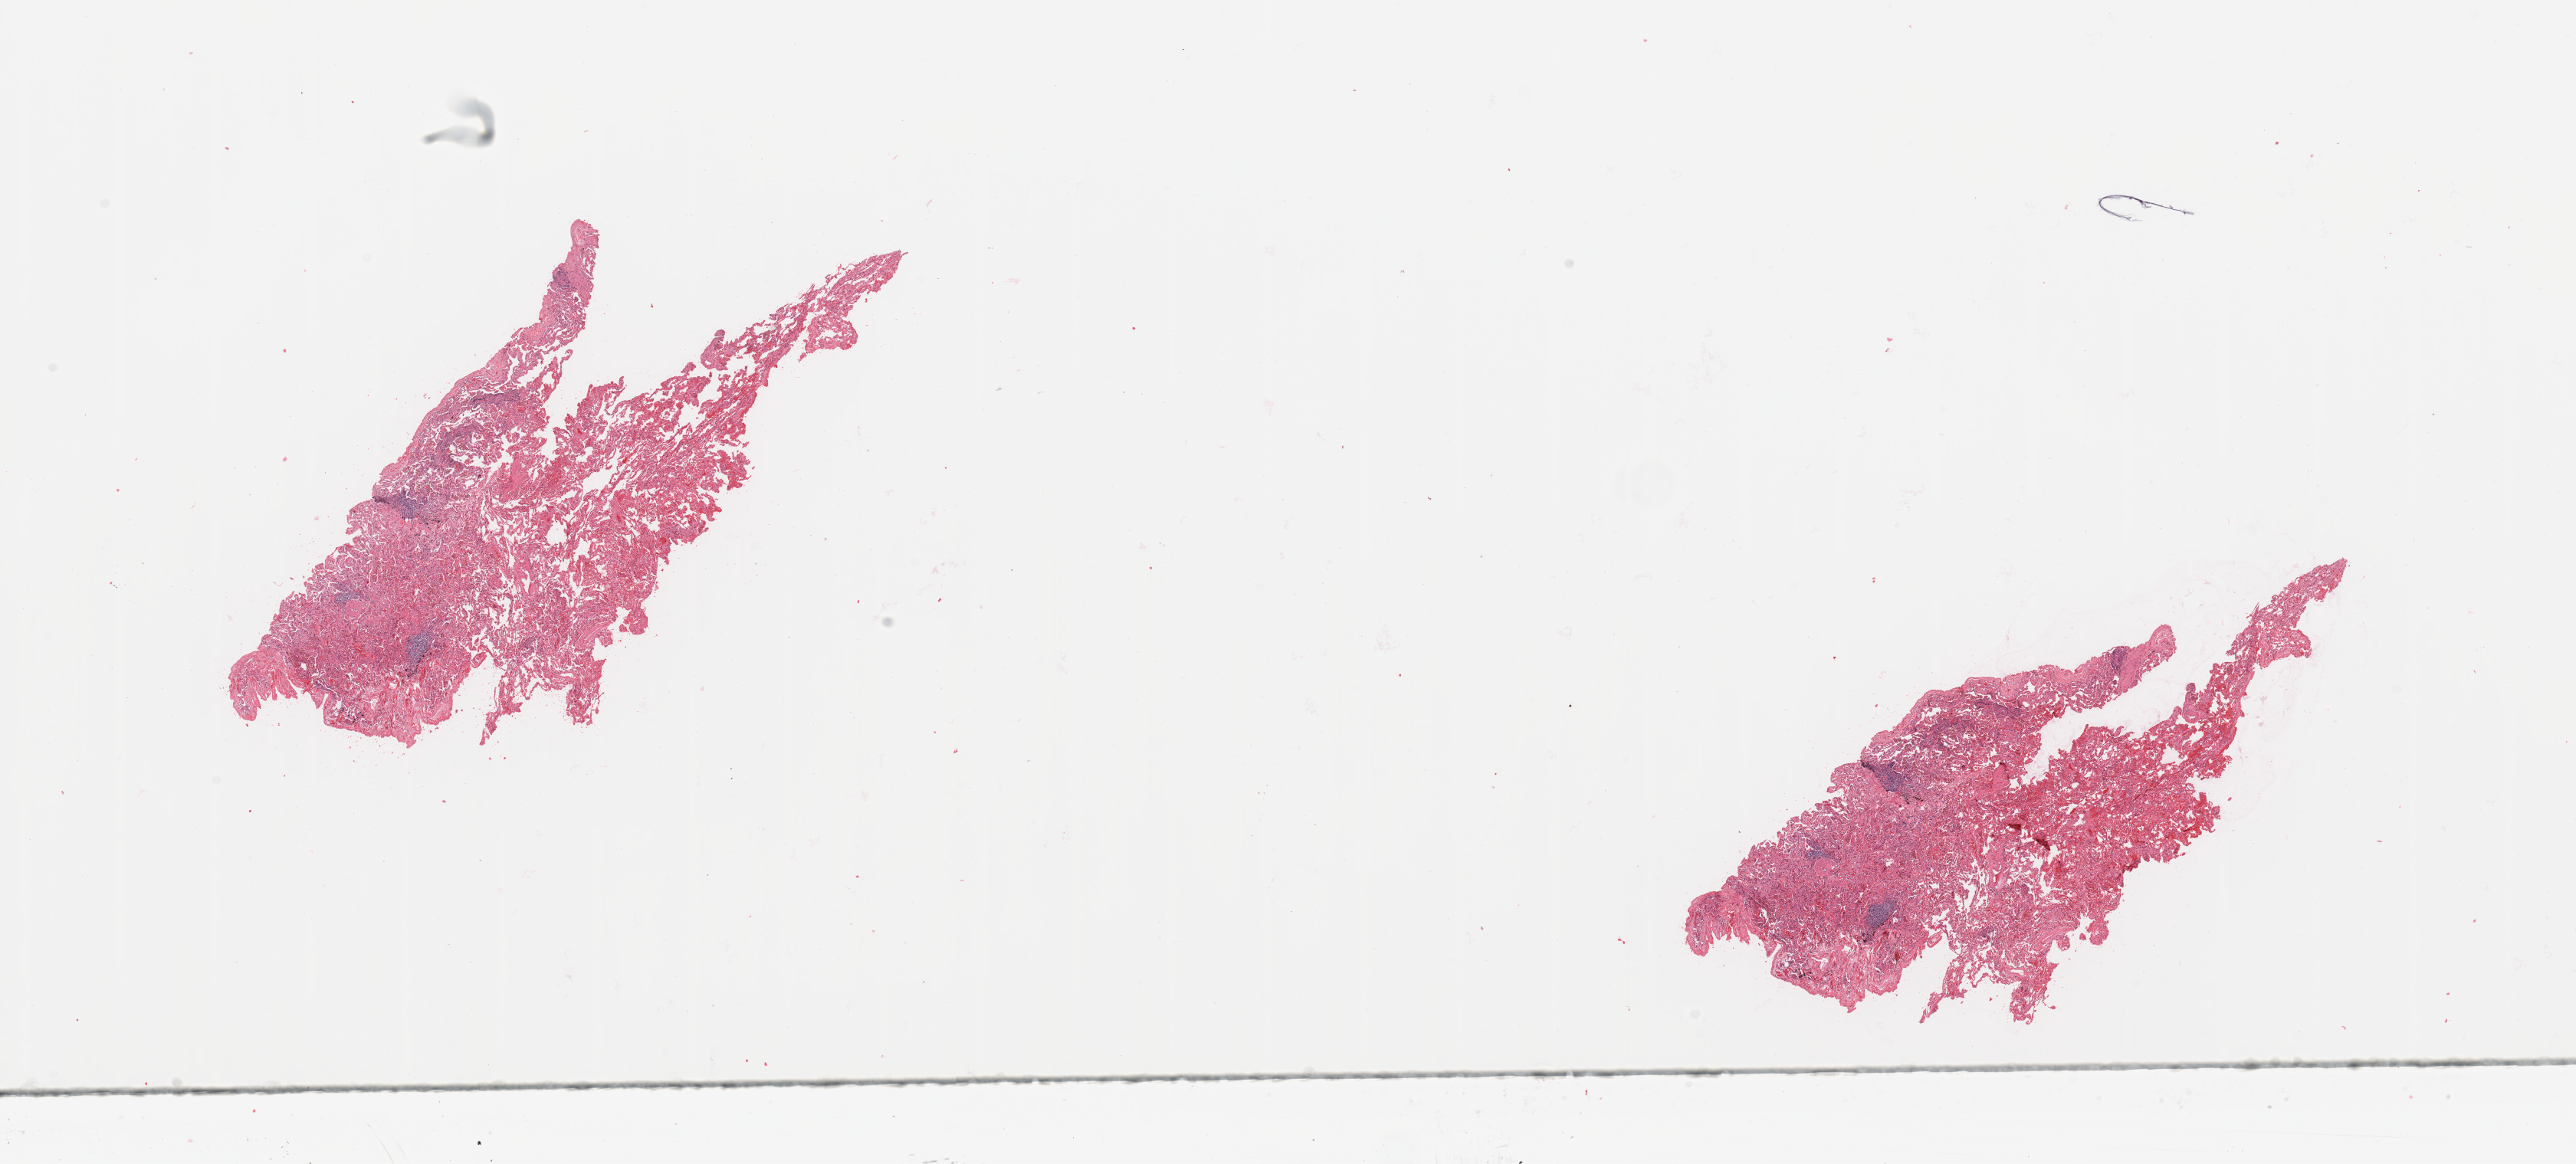
Whole-slide histology image, Hematoxylin and eosin (H&E) stained, a low-resolution overview of the entire scanned area, about 26.6 x 12.0 mm (acquisition: 20x scan); lung, normal (non-tumour) tissue. 64-year-old female patient.
This section: normal (non-tumour) tissue from the same patient. Patient diagnosis: Squamous cell carcinoma, NOS.